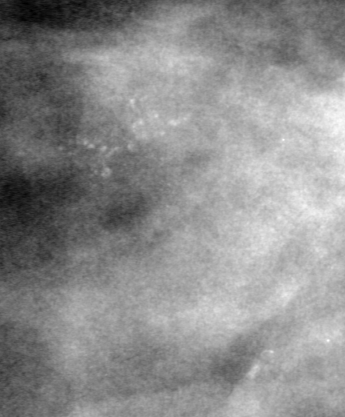
Cropped region of a digitized screen-film mammogram centred on a radiologist-marked abnormality; left breast; CC view.
- Calcifications, morphology pleomorphic, distribution clustered; BI-RADS assessment category 4; pathology (as recorded): benign.